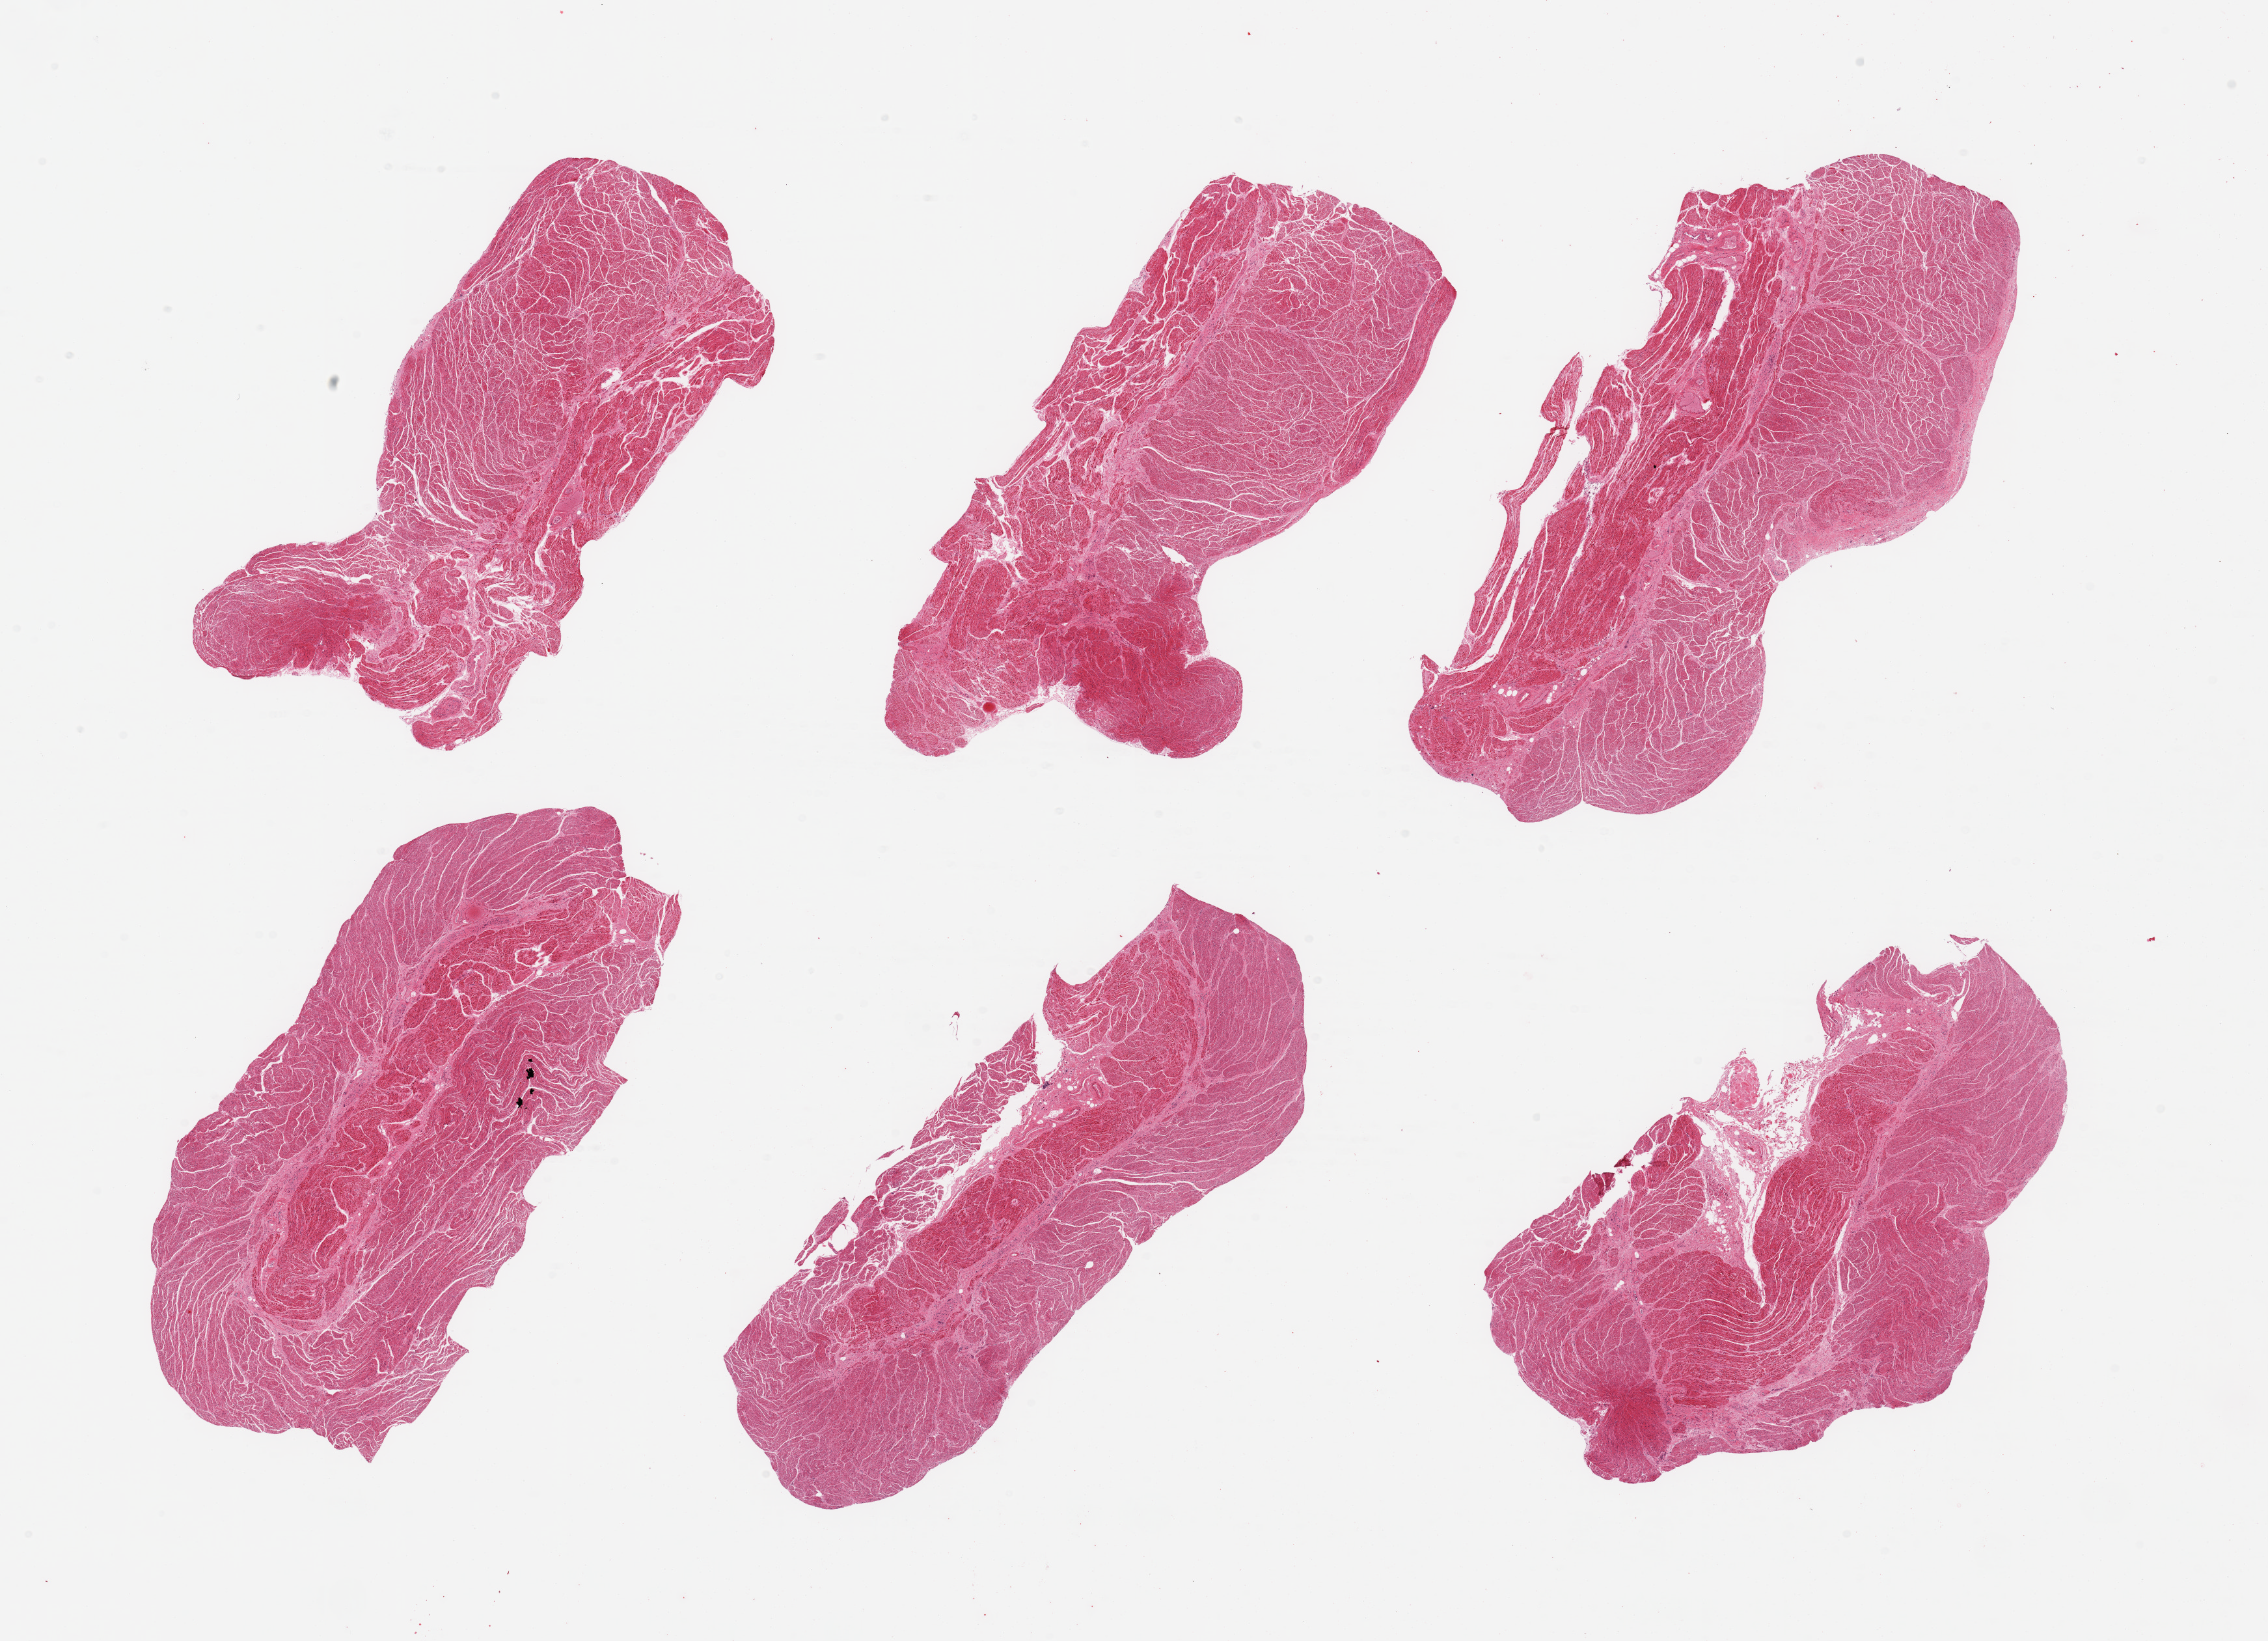
Digitized haematoxylin and eosin-stained section — a low-resolution overview of the entire scanned area, about 27.6 x 19.9 mm; PAXgene-fixed, paraffin-embedded tissue; sampled site (target tissue): gastroesophageal junction; tissue donor sample. Male donor.
• pathologist's review note for this sample: 6 pieces, confirmed target muscularis